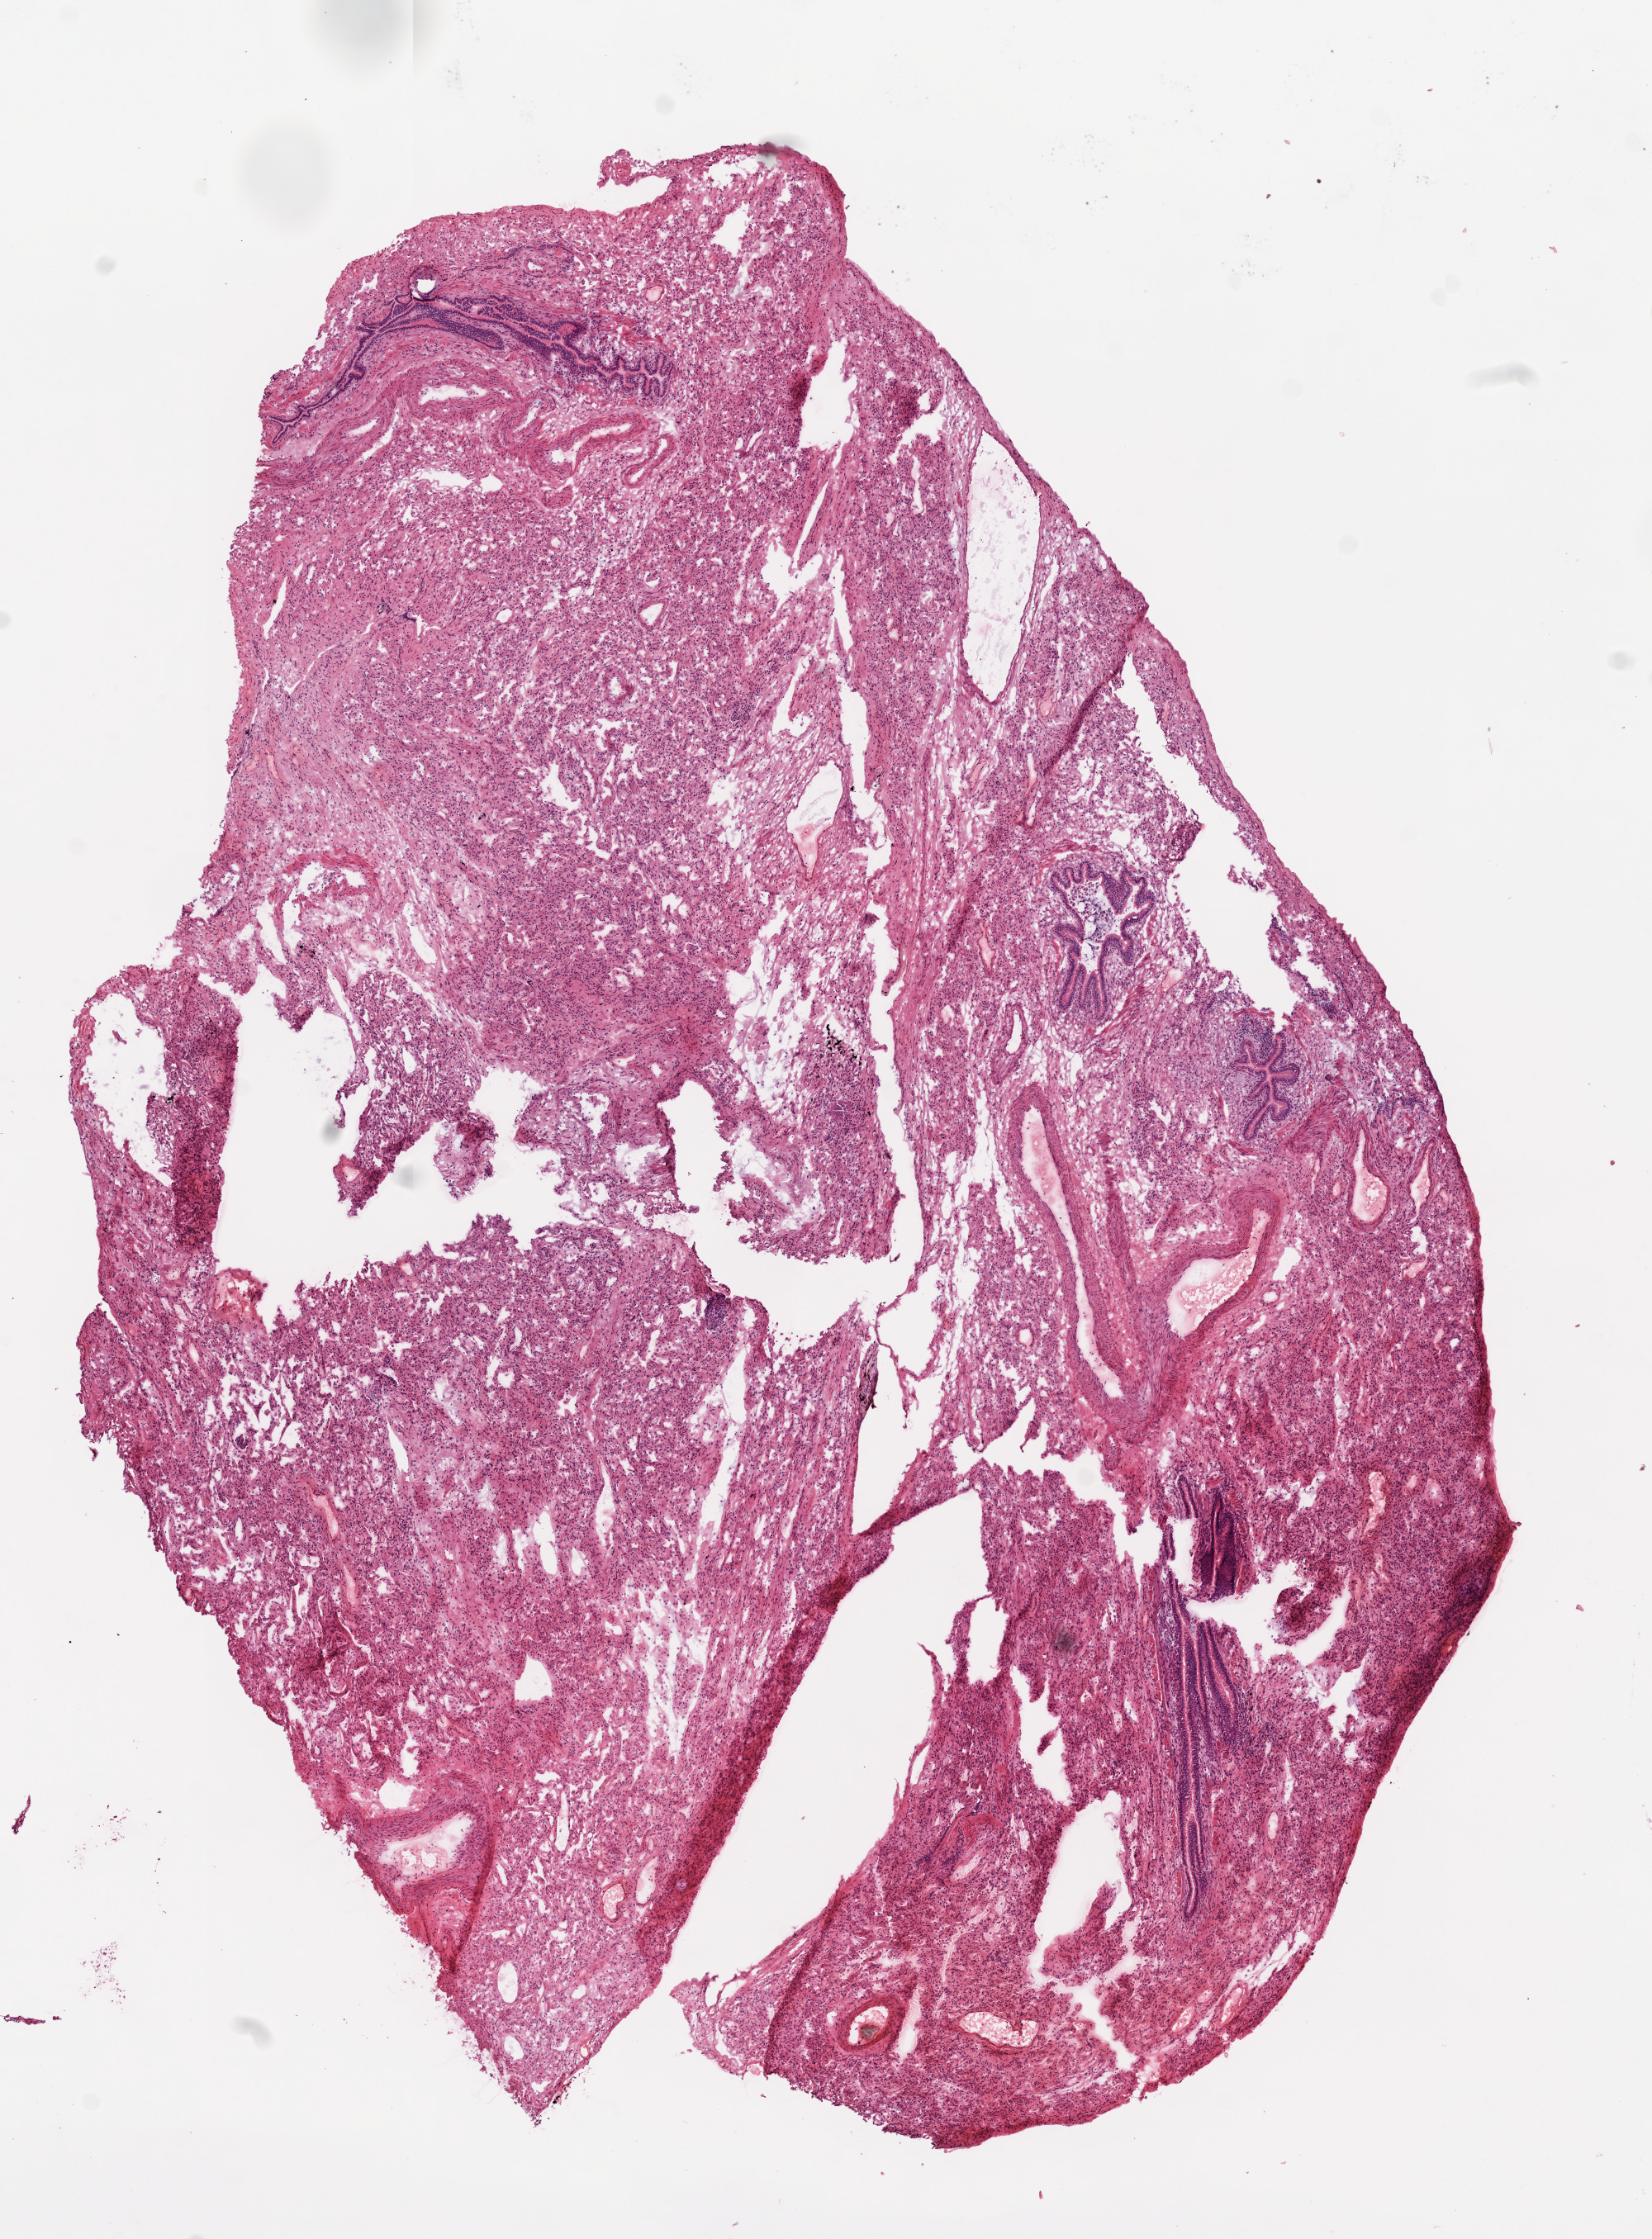
H&E whole-slide image, shown as a low-resolution overview of the whole scanned area (about 8.0 x 10.9 mm, acquisition: 20x scan), frozen section, solid tissue normal (non-tumour tissue) sample from the lung. Female, age 68 years at initial diagnosis.
- this section: solid tissue normal (non-tumour) sample from the same patient
- patient diagnosis: Adenocarcinoma, NOS (upper lobe, lung)